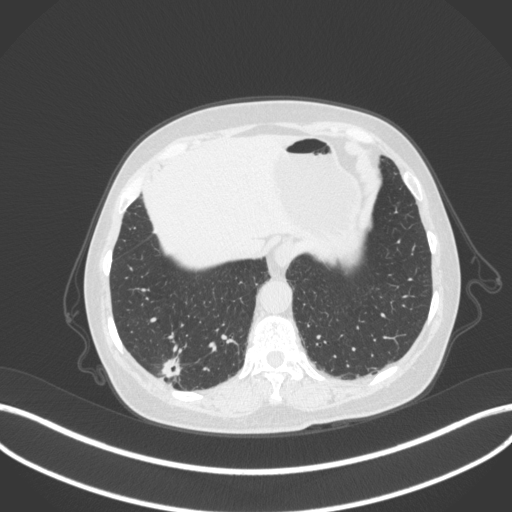
Chest CT, one axial slice; position 55 of 340 along the scan axis; lung window (W 1500 / L -600 HU); 1 mm slice thickness; 512 × 512 image matrix. Female patient, age 69 years. From the clinical record (not read from this slice): clinical TNM (as recorded): T1b N0 M0.
Annotated regions visible in this slice (rectangle marked by the reading radiologist):
- lung tumour (recorded histology: adenocarcinoma): box from (x=155, y=353) to (x=183, y=380) px